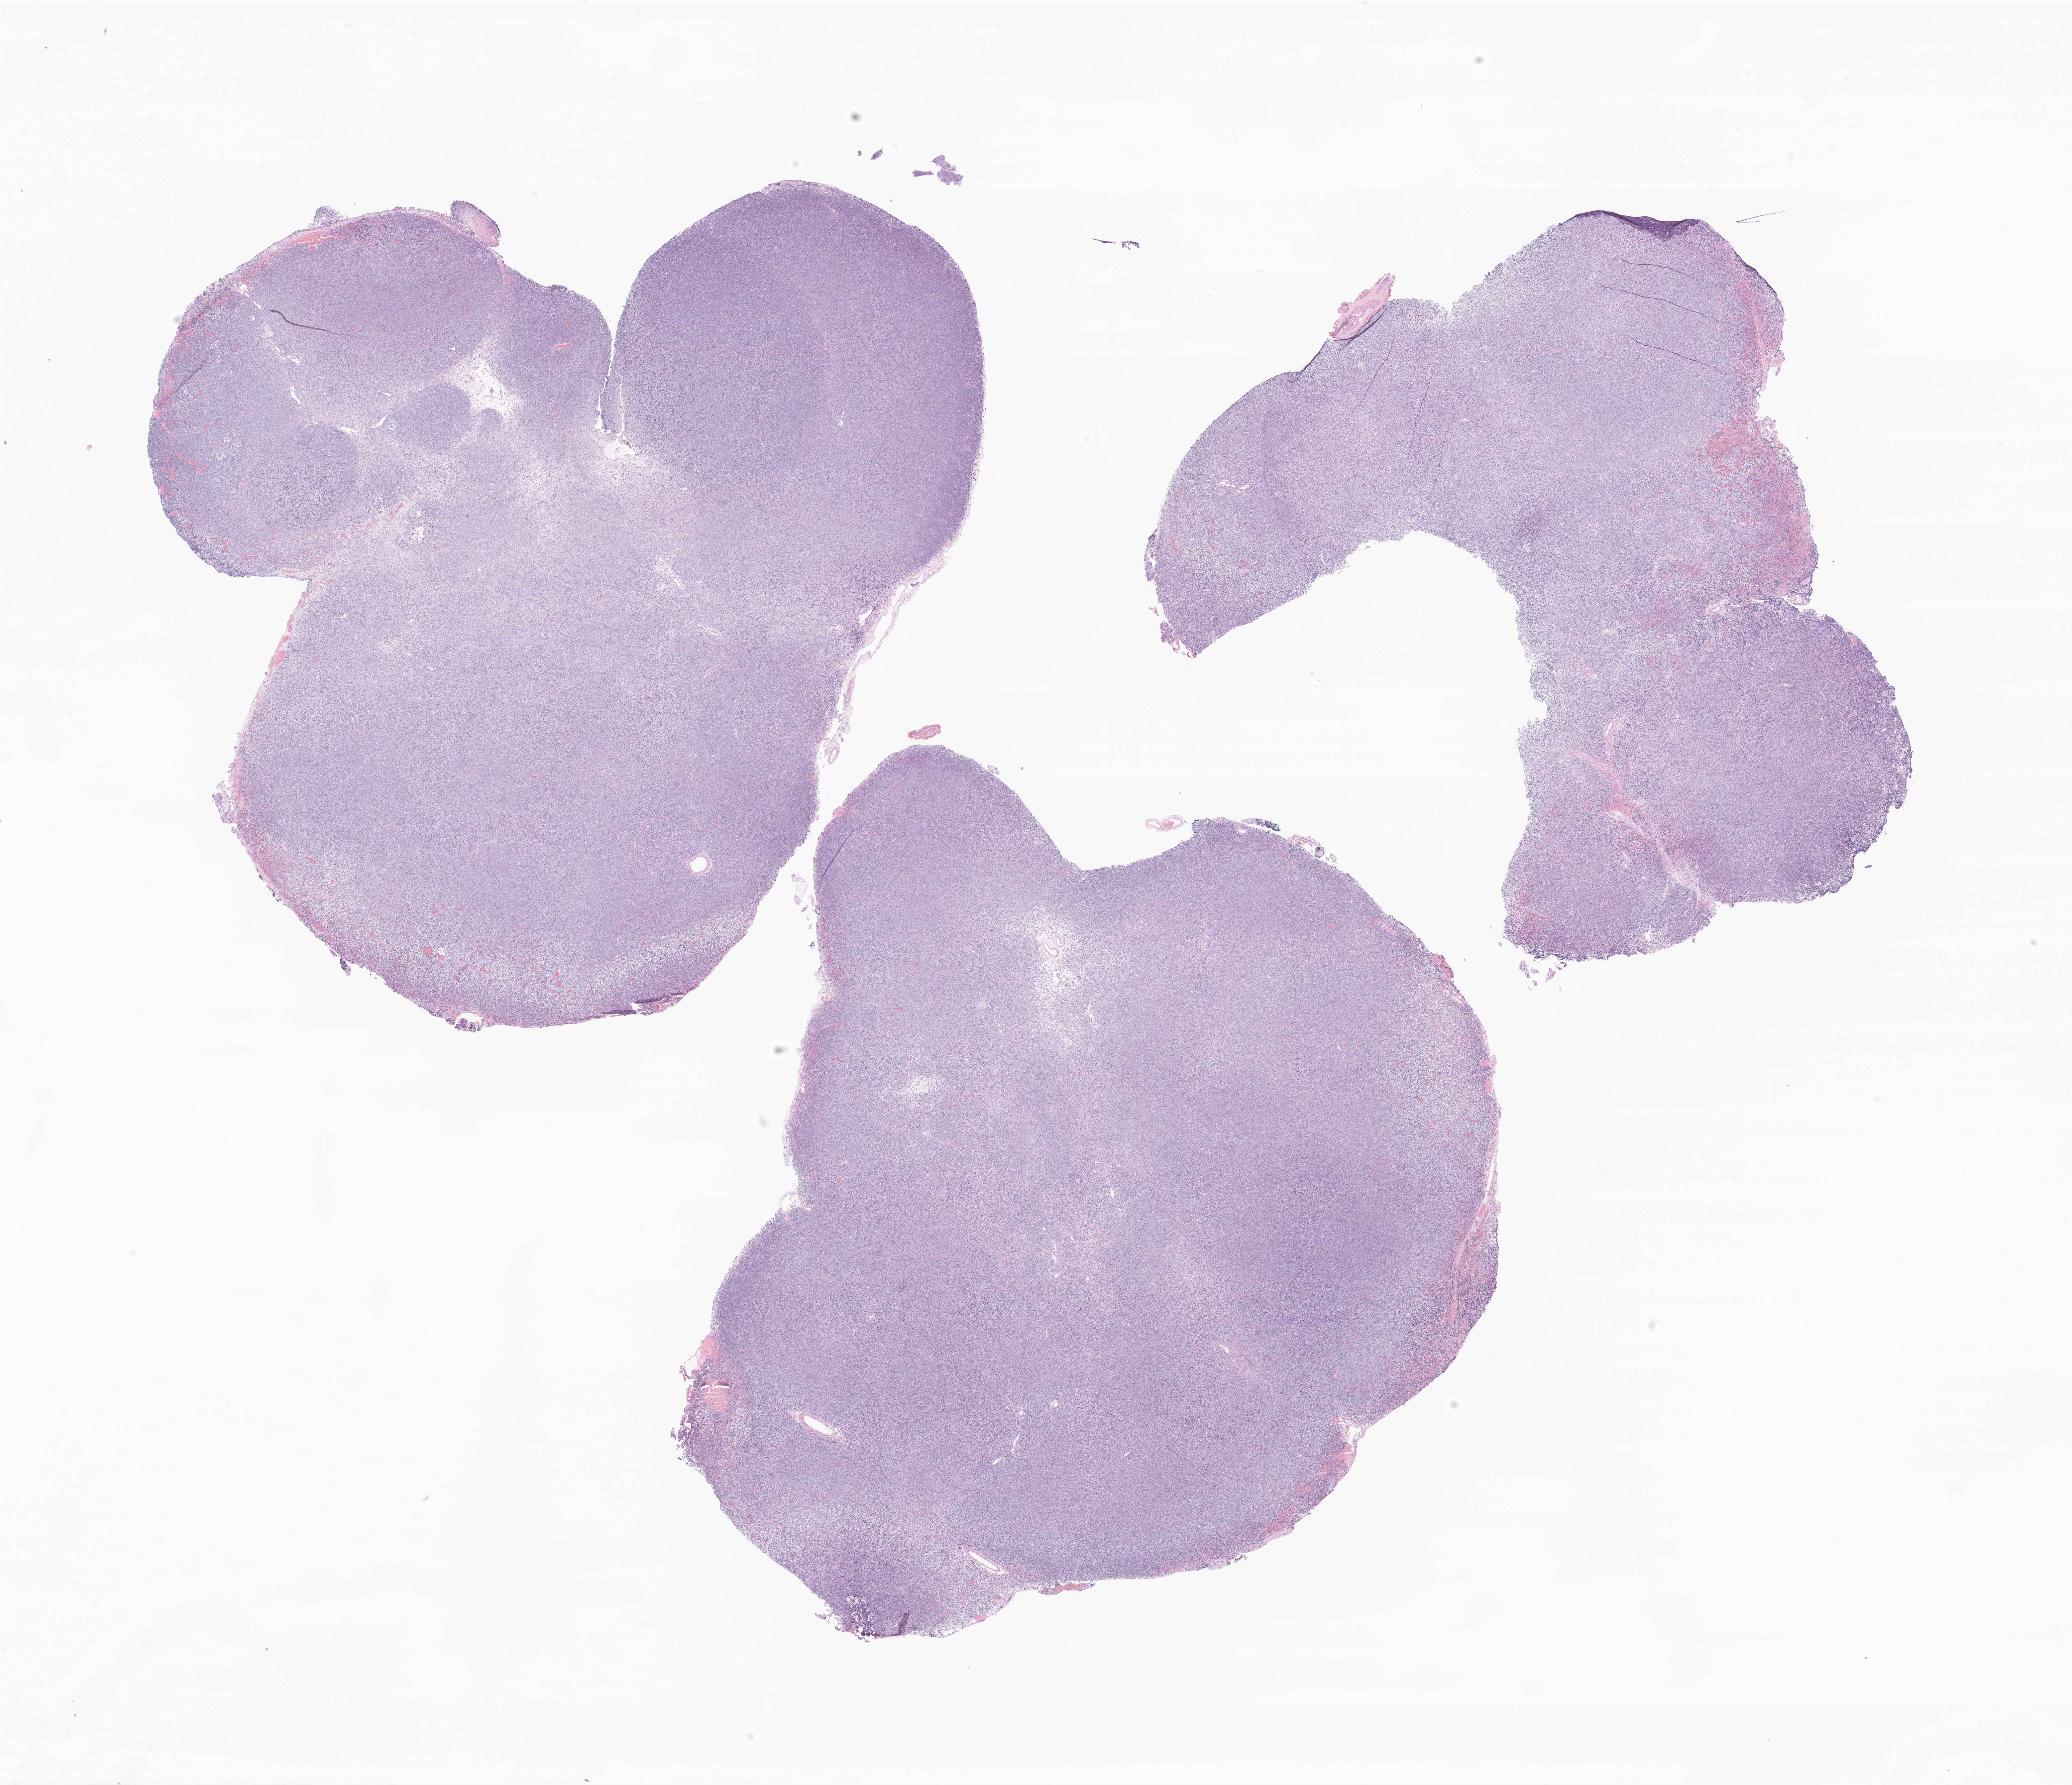
H&E whole-slide image of tumor tissue from the brain, shown as a low-resolution overview of the whole scanned area (about 26.3 x 22.6 mm); formalin-fixed paraffin-embedded section. Male patient, age 355 days.
* diagnosis (ICD-O-3 morphology term): Neoplasm, malignant